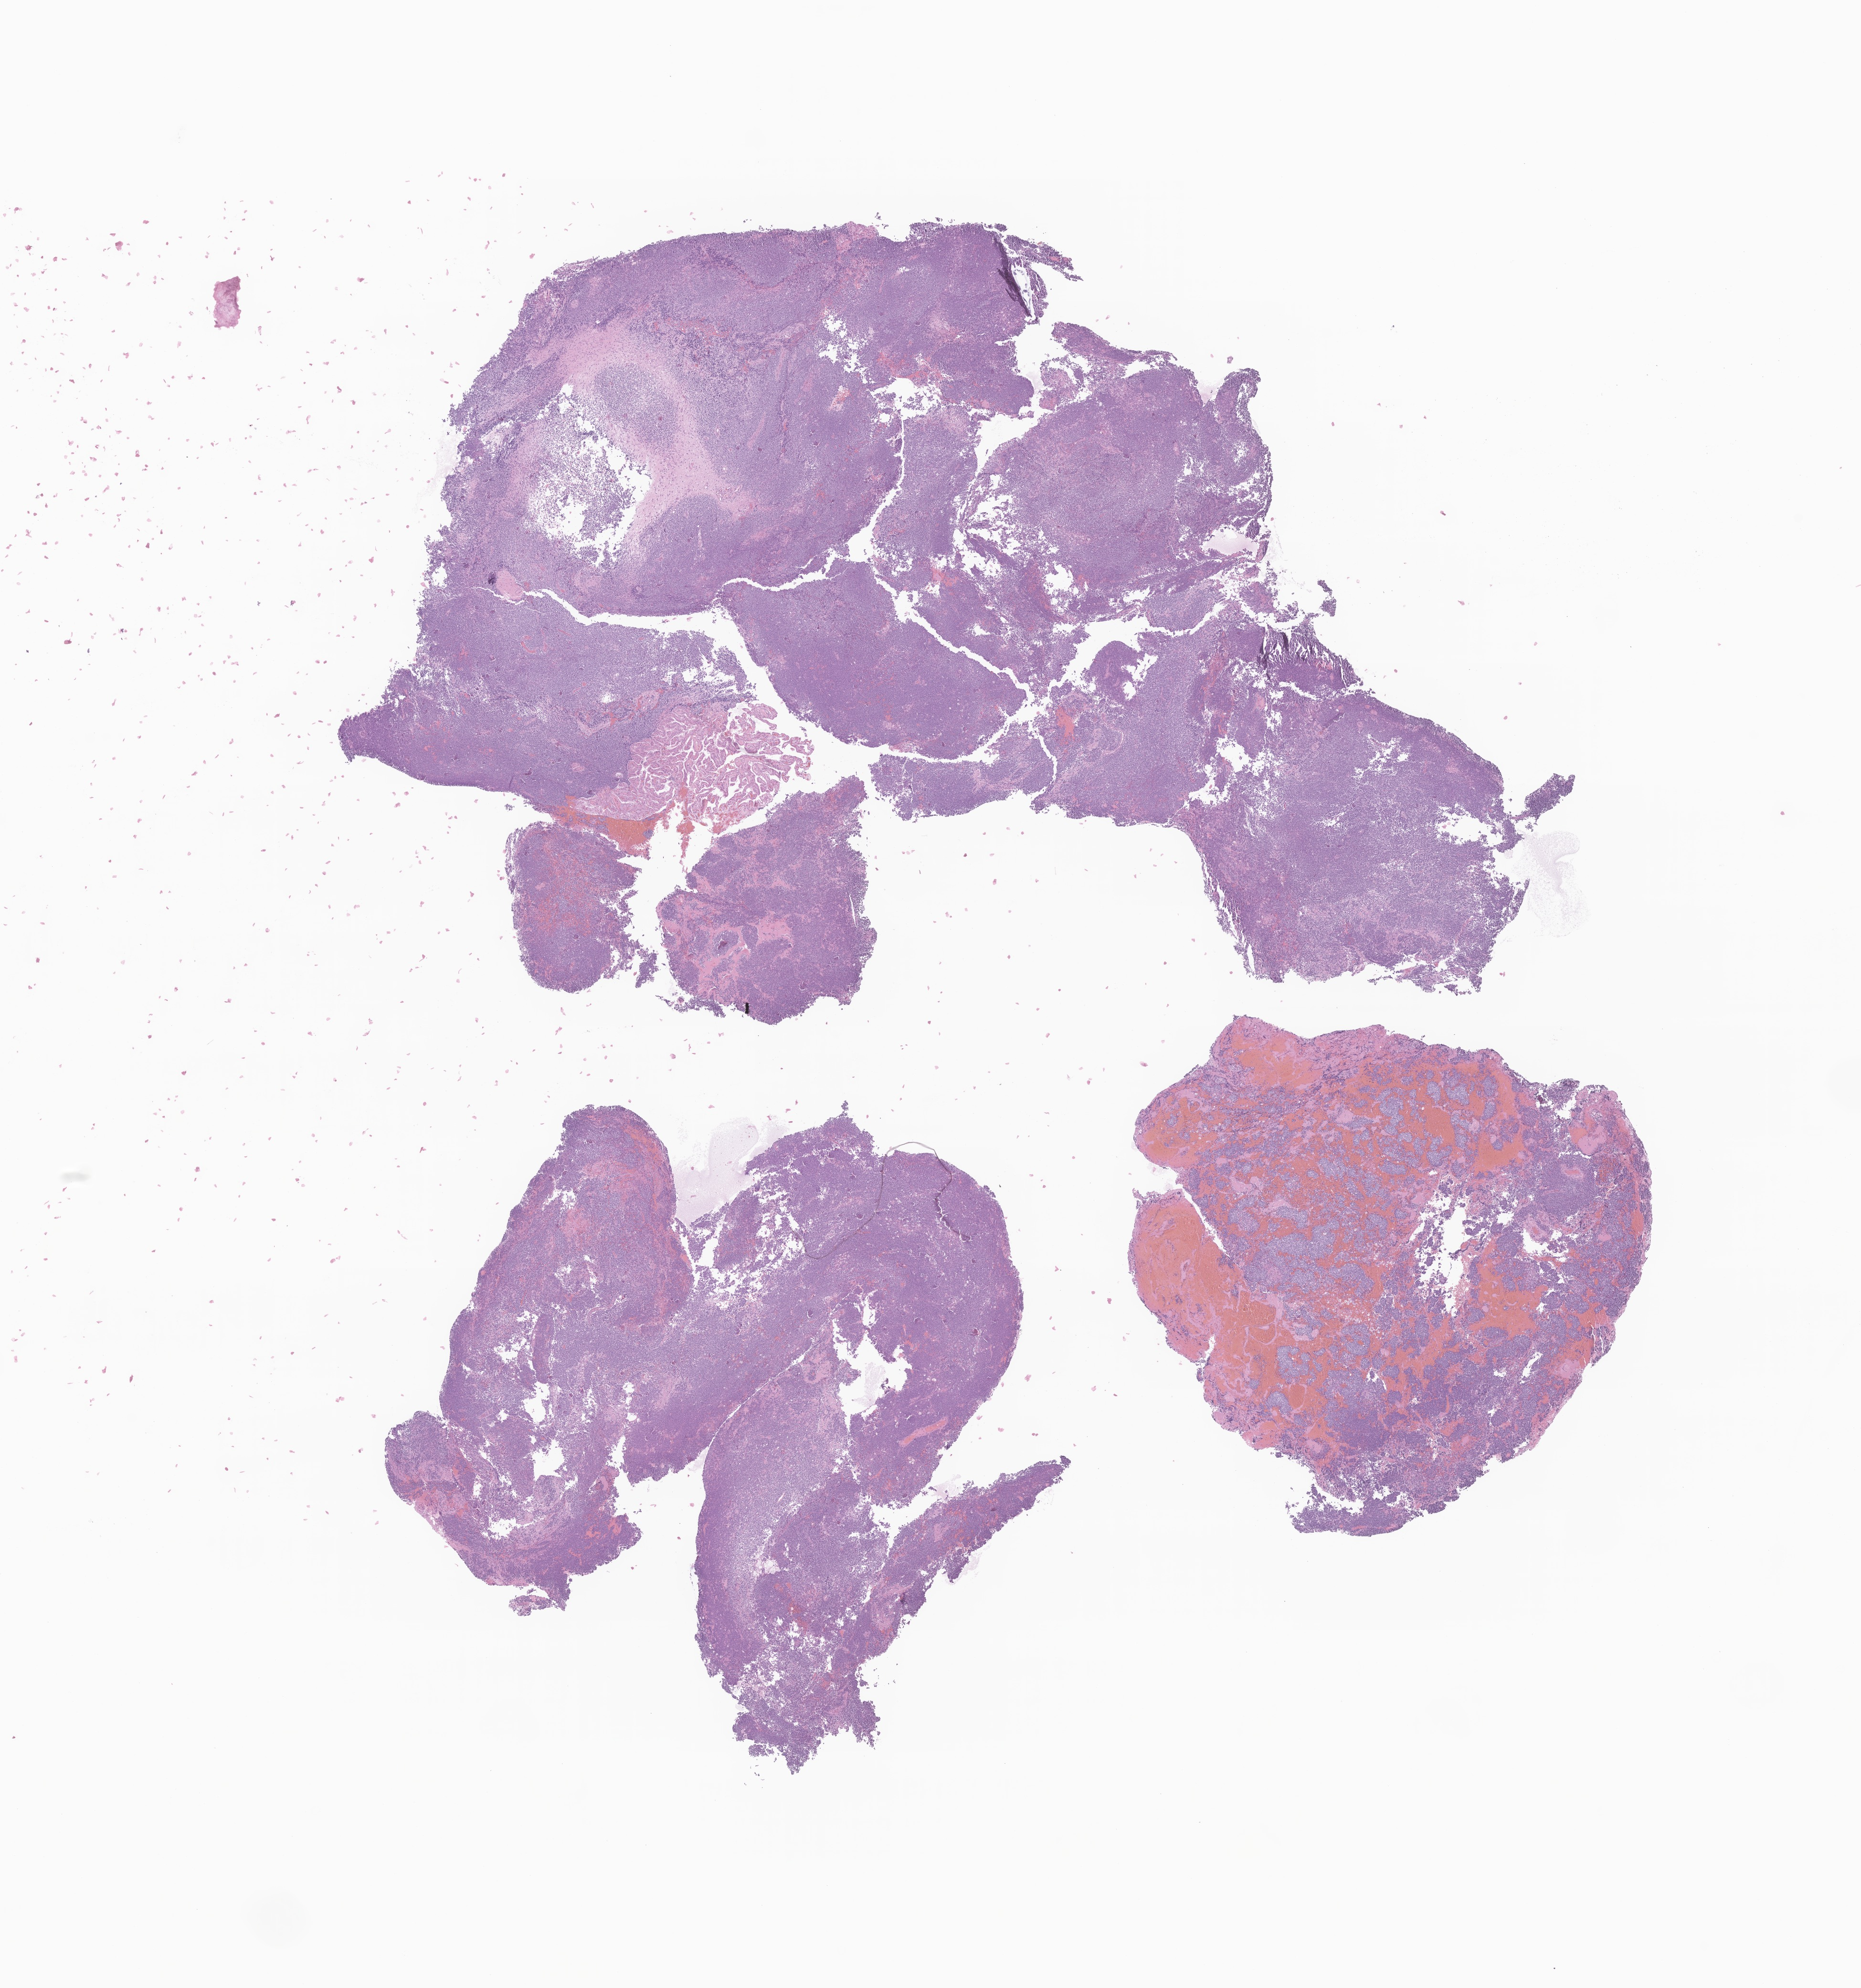
Hematoxylin and eosin (H&E) whole-slide image of tumor tissue from the brain — shown as a low-resolution overview of the whole scanned area (about 16.4 x 17.6 mm), formalin-fixed, paraffin-embedded (FFPE) tissue. Patient: female, age 87 months (7 years 3 months).
Recorded diagnosis: Medulloblastoma, NOS.